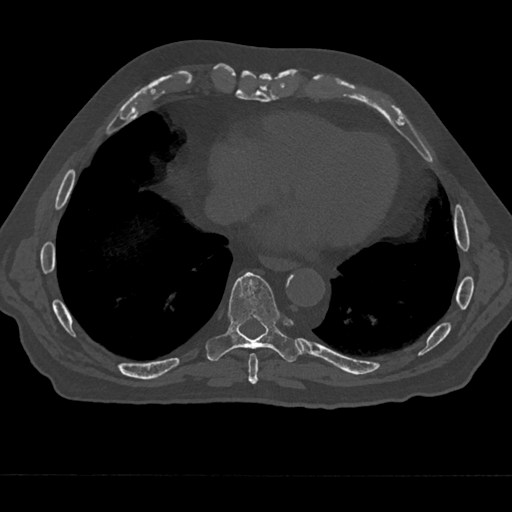
CT including the spine, one axial slice; slice 271 of 797 in the series (ordered by position); 120 kVp; bone window (W 1800 / L 400 HU); 512 × 512 image matrix. Patient: male, 75 years. From the clinical record (not read from this slice): primary cancer: renal.
Annotated regions visible in this slice (semi-automatically segmented with operator editing):
- T8 vertebra: bounding box [x1, y1, x2, y2] px = [248, 353, 258, 385]
- T9 vertebra: [205, 272, 302, 362]